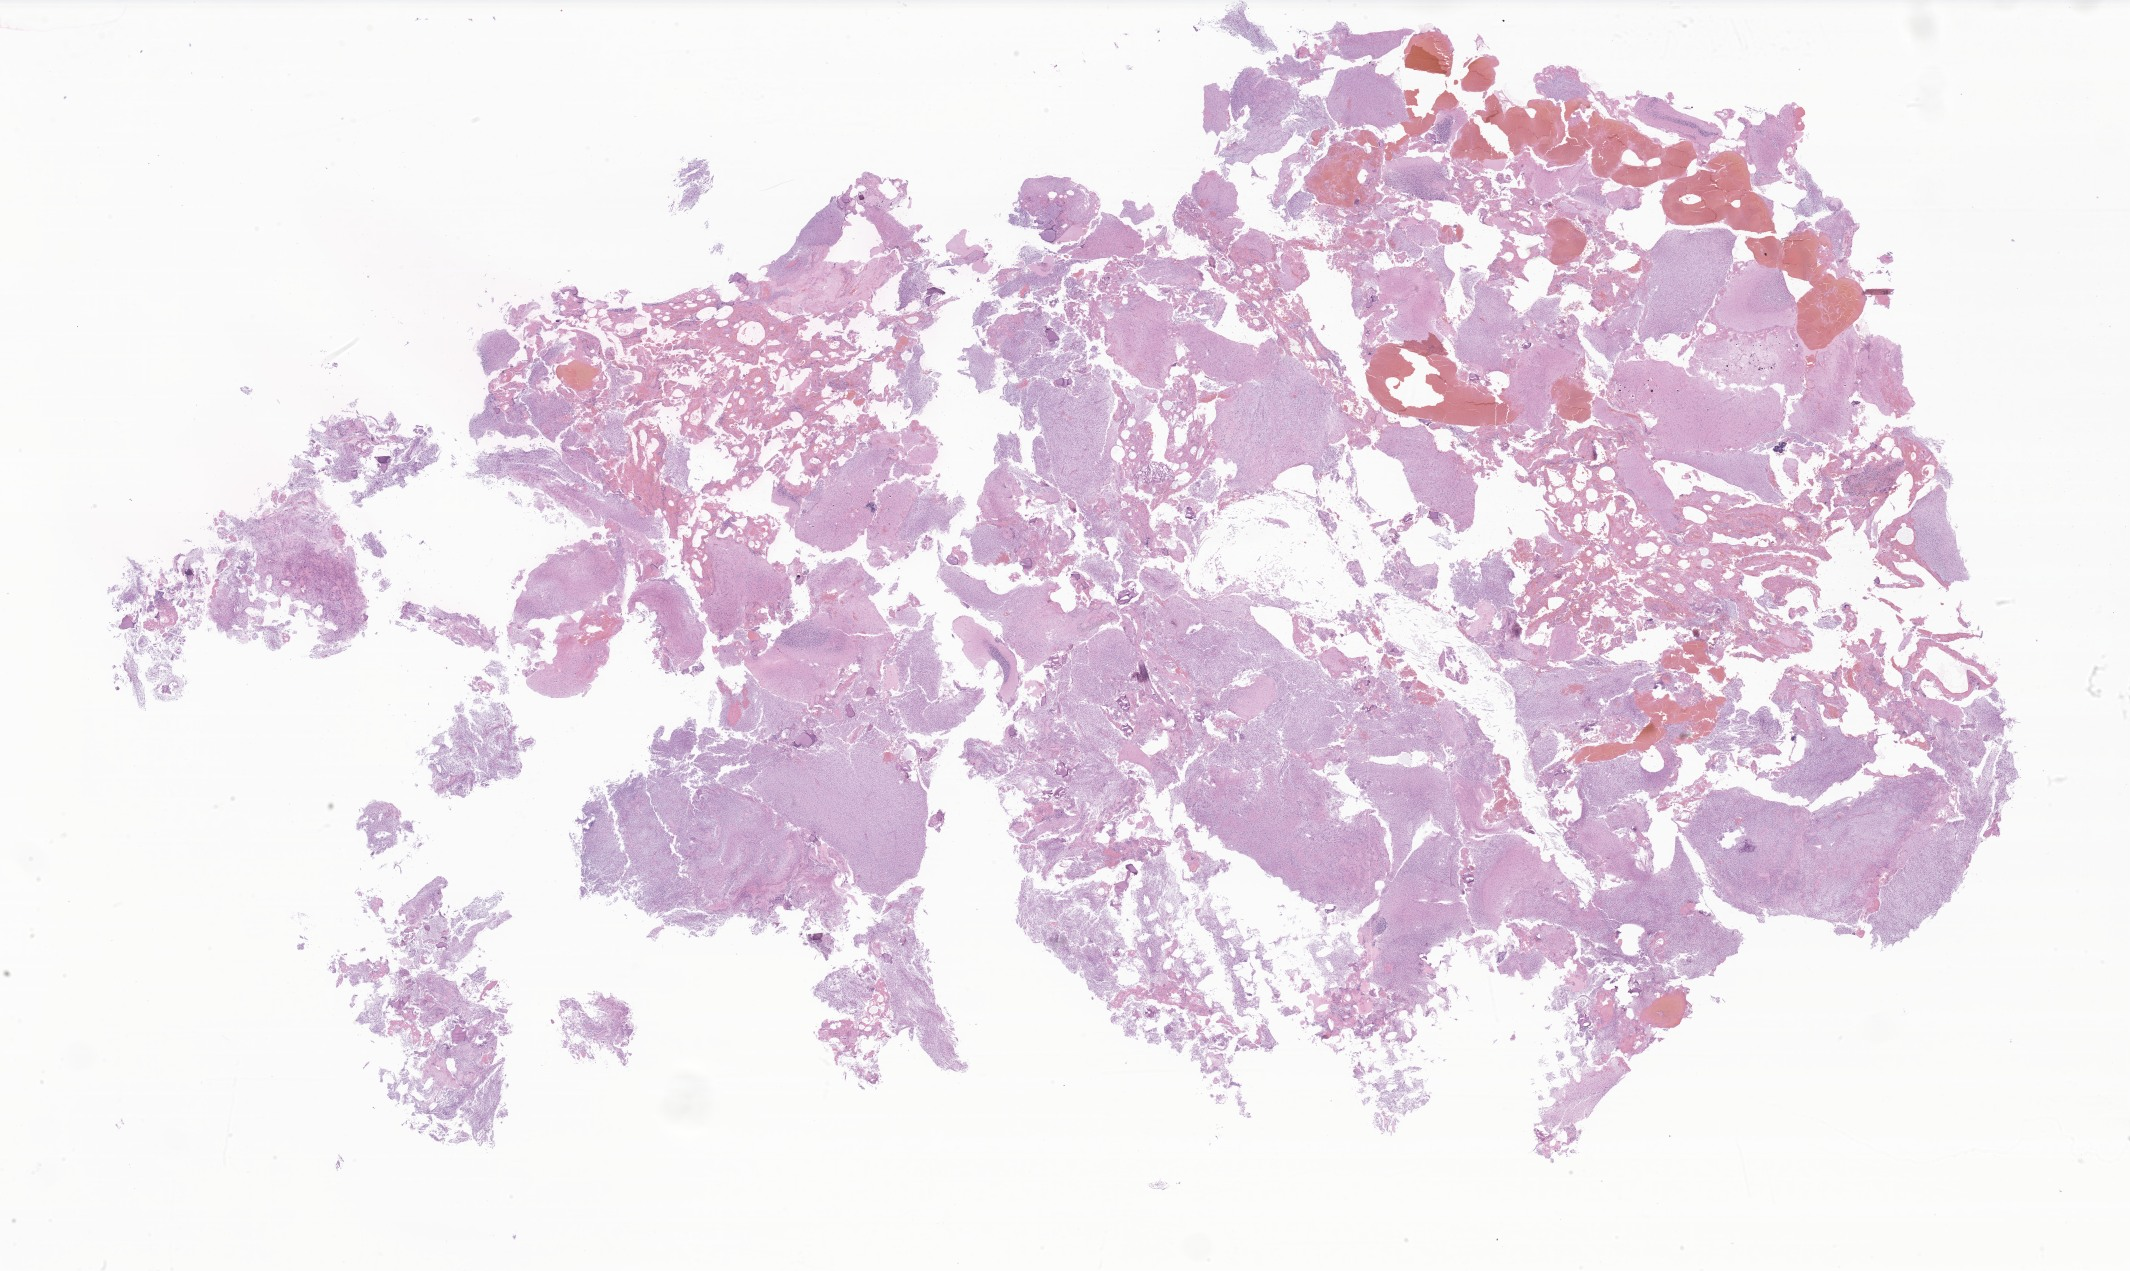
Hematoxylin and eosin (H&E) whole-slide image of tumor tissue from the cranial nerve, whole scanned area (about 35.9 x 21.4 mm) shown as a low-resolution overview. FFPE section. Patient male; age 75 months (6 years 3 months).
Diagnosis (ICD-O-3 morphology term): Pilocytic astrocytoma.